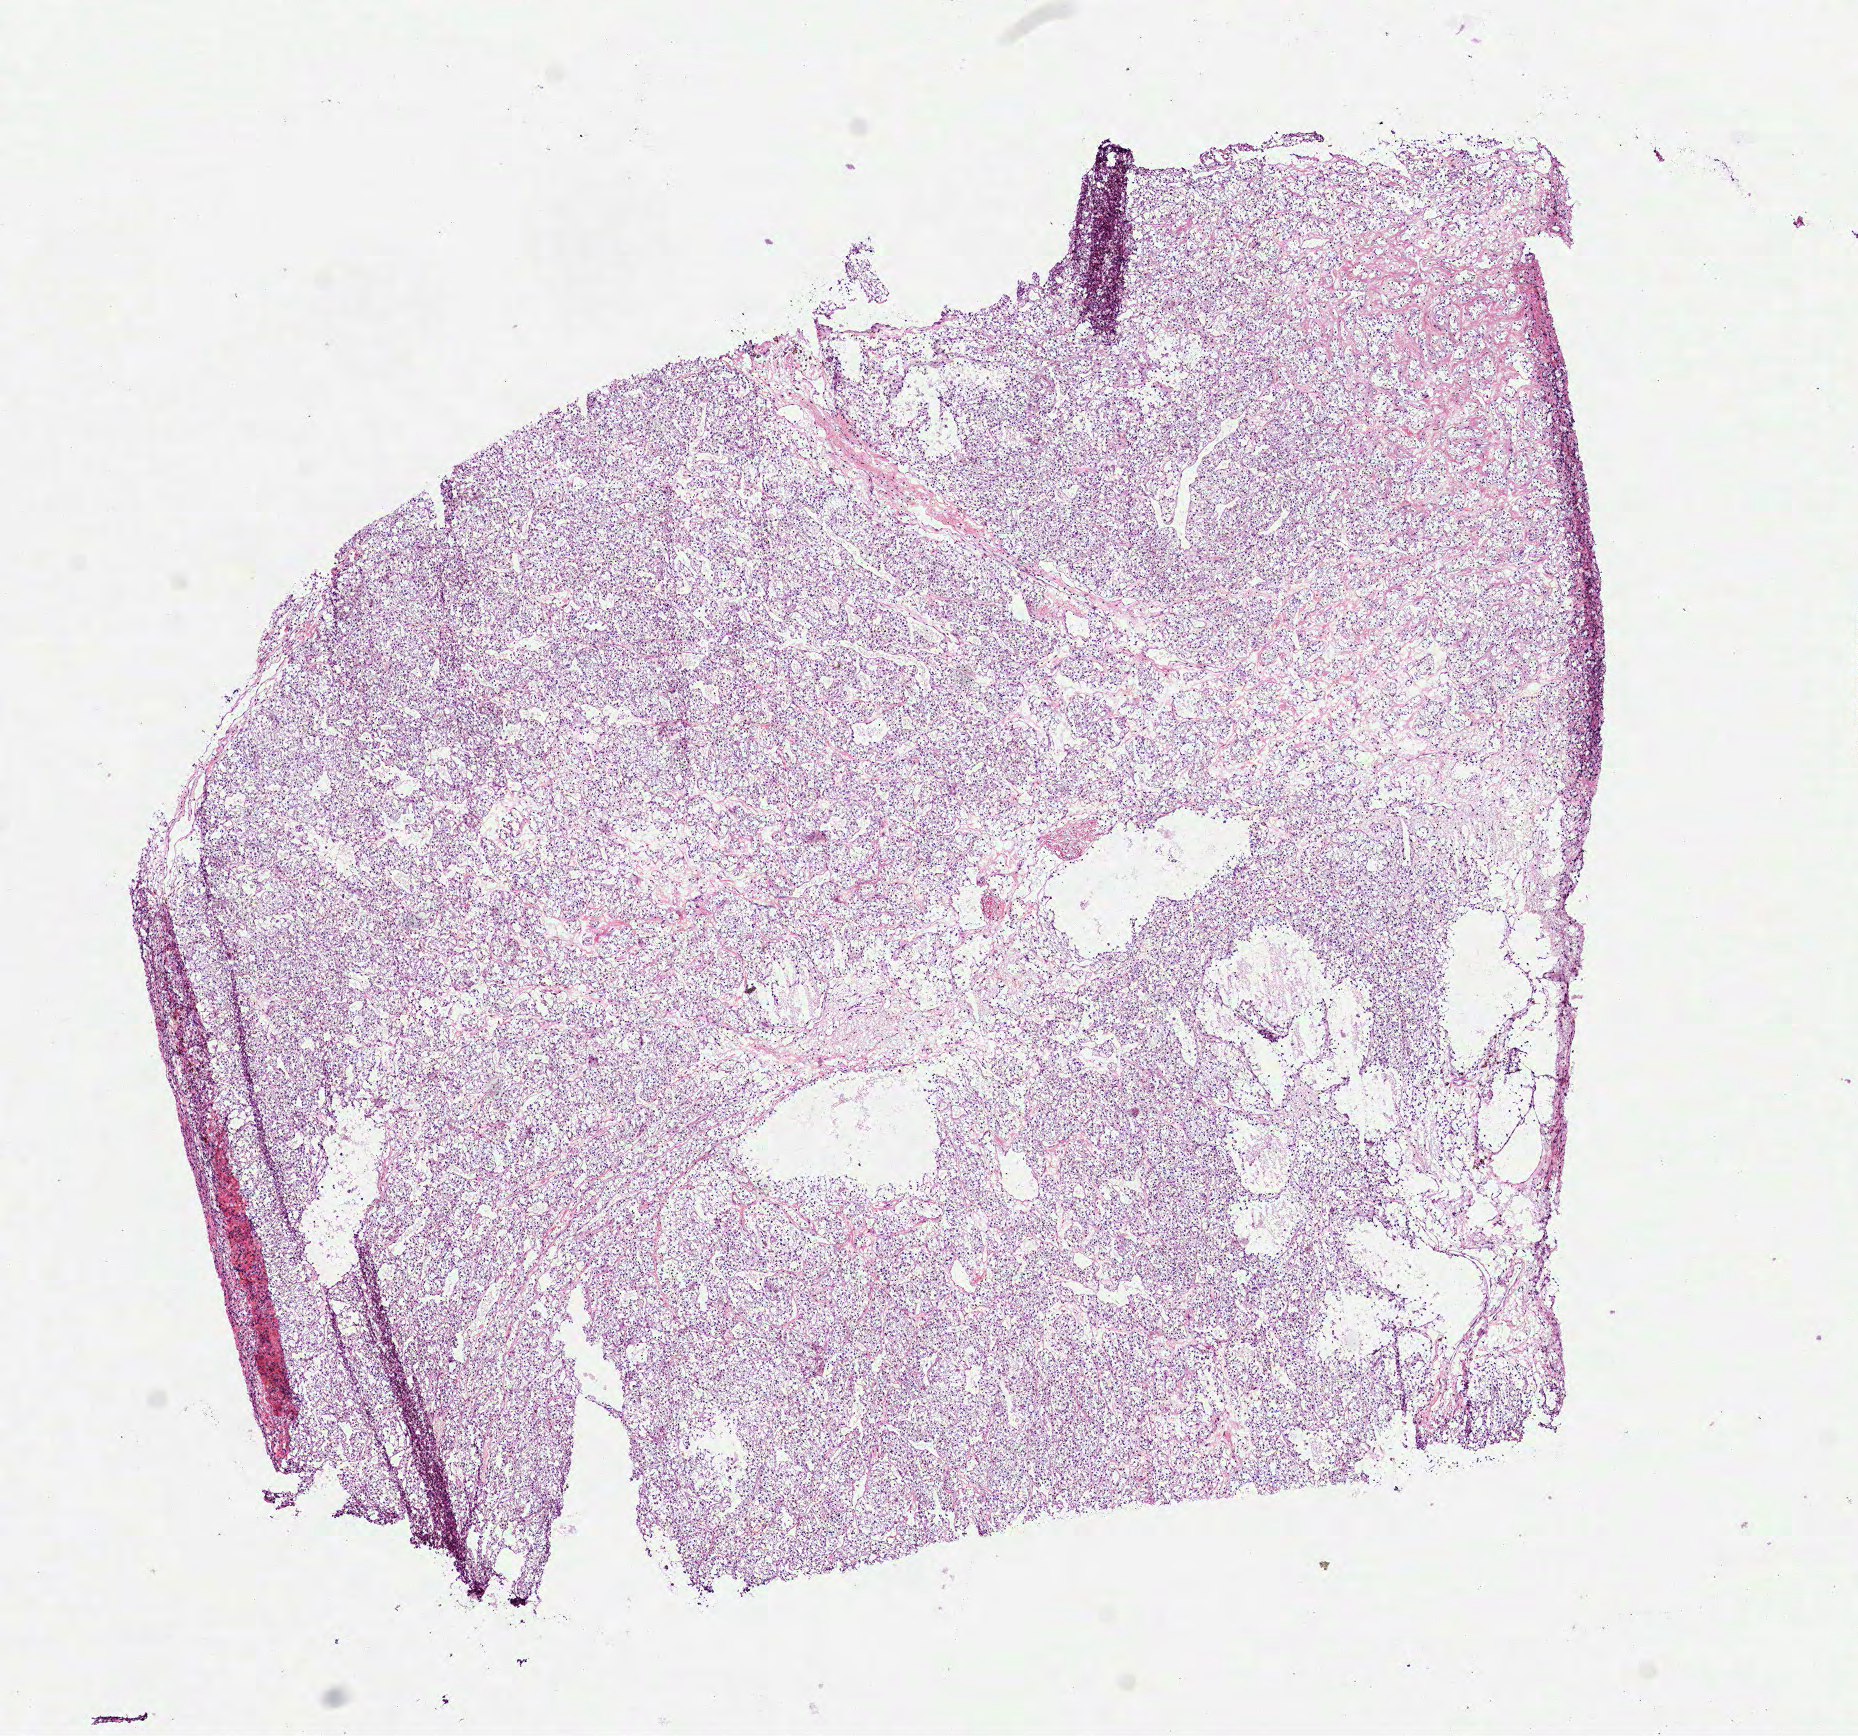
Digitized H&E-stained tissue section (whole slide), low-resolution overview of the scanned area, about 7.5 x 7.0 mm (slide scanned at 40x), frozen section from the top of the tissue portion, sample: primary tumour, kidney. Patient: female, age at initial diagnosis 41 years. Histologic grade: G2 (moderately differentiated). Pathologist review of this section (percent, as recorded): tumour cells 95%, tumour nuclei 85%, normal cells 0%, stromal cells 5%, necrosis 0%.
Pathologic diagnosis: Clear cell adenocarcinoma, NOS. AJCC pathologic stage: I (6th edition). Laterality: right.